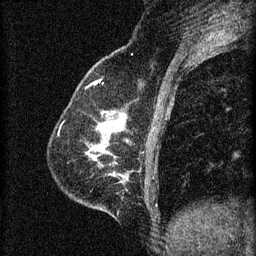
Breast MRI (dynamic contrast-enhanced), one sagittal slice; position 22 of 60 along the scan axis; 3 images stored at this slice position (order not interpretable as contrast timing); 1.5 T; TE 4.2 ms, TR 8.2 ms; 2 mm slice thickness; 256 × 256 image matrix, field of view 180 × 180 mm. Female patient, age 59 years.
Structures marked on this image (semi-automatic segmentation, software-assisted and operator-edited):
- analysis volume of interest (the breast-tissue region the enhancement analysis was run in; not a lesion): bounding box (x1, y1, x2, y2) in pixels: (67, 104, 130, 161)
- tumour enhancement mask (voxels above the 70 % enhancement threshold inside the analysis volume of interest): (98, 112, 121, 133)